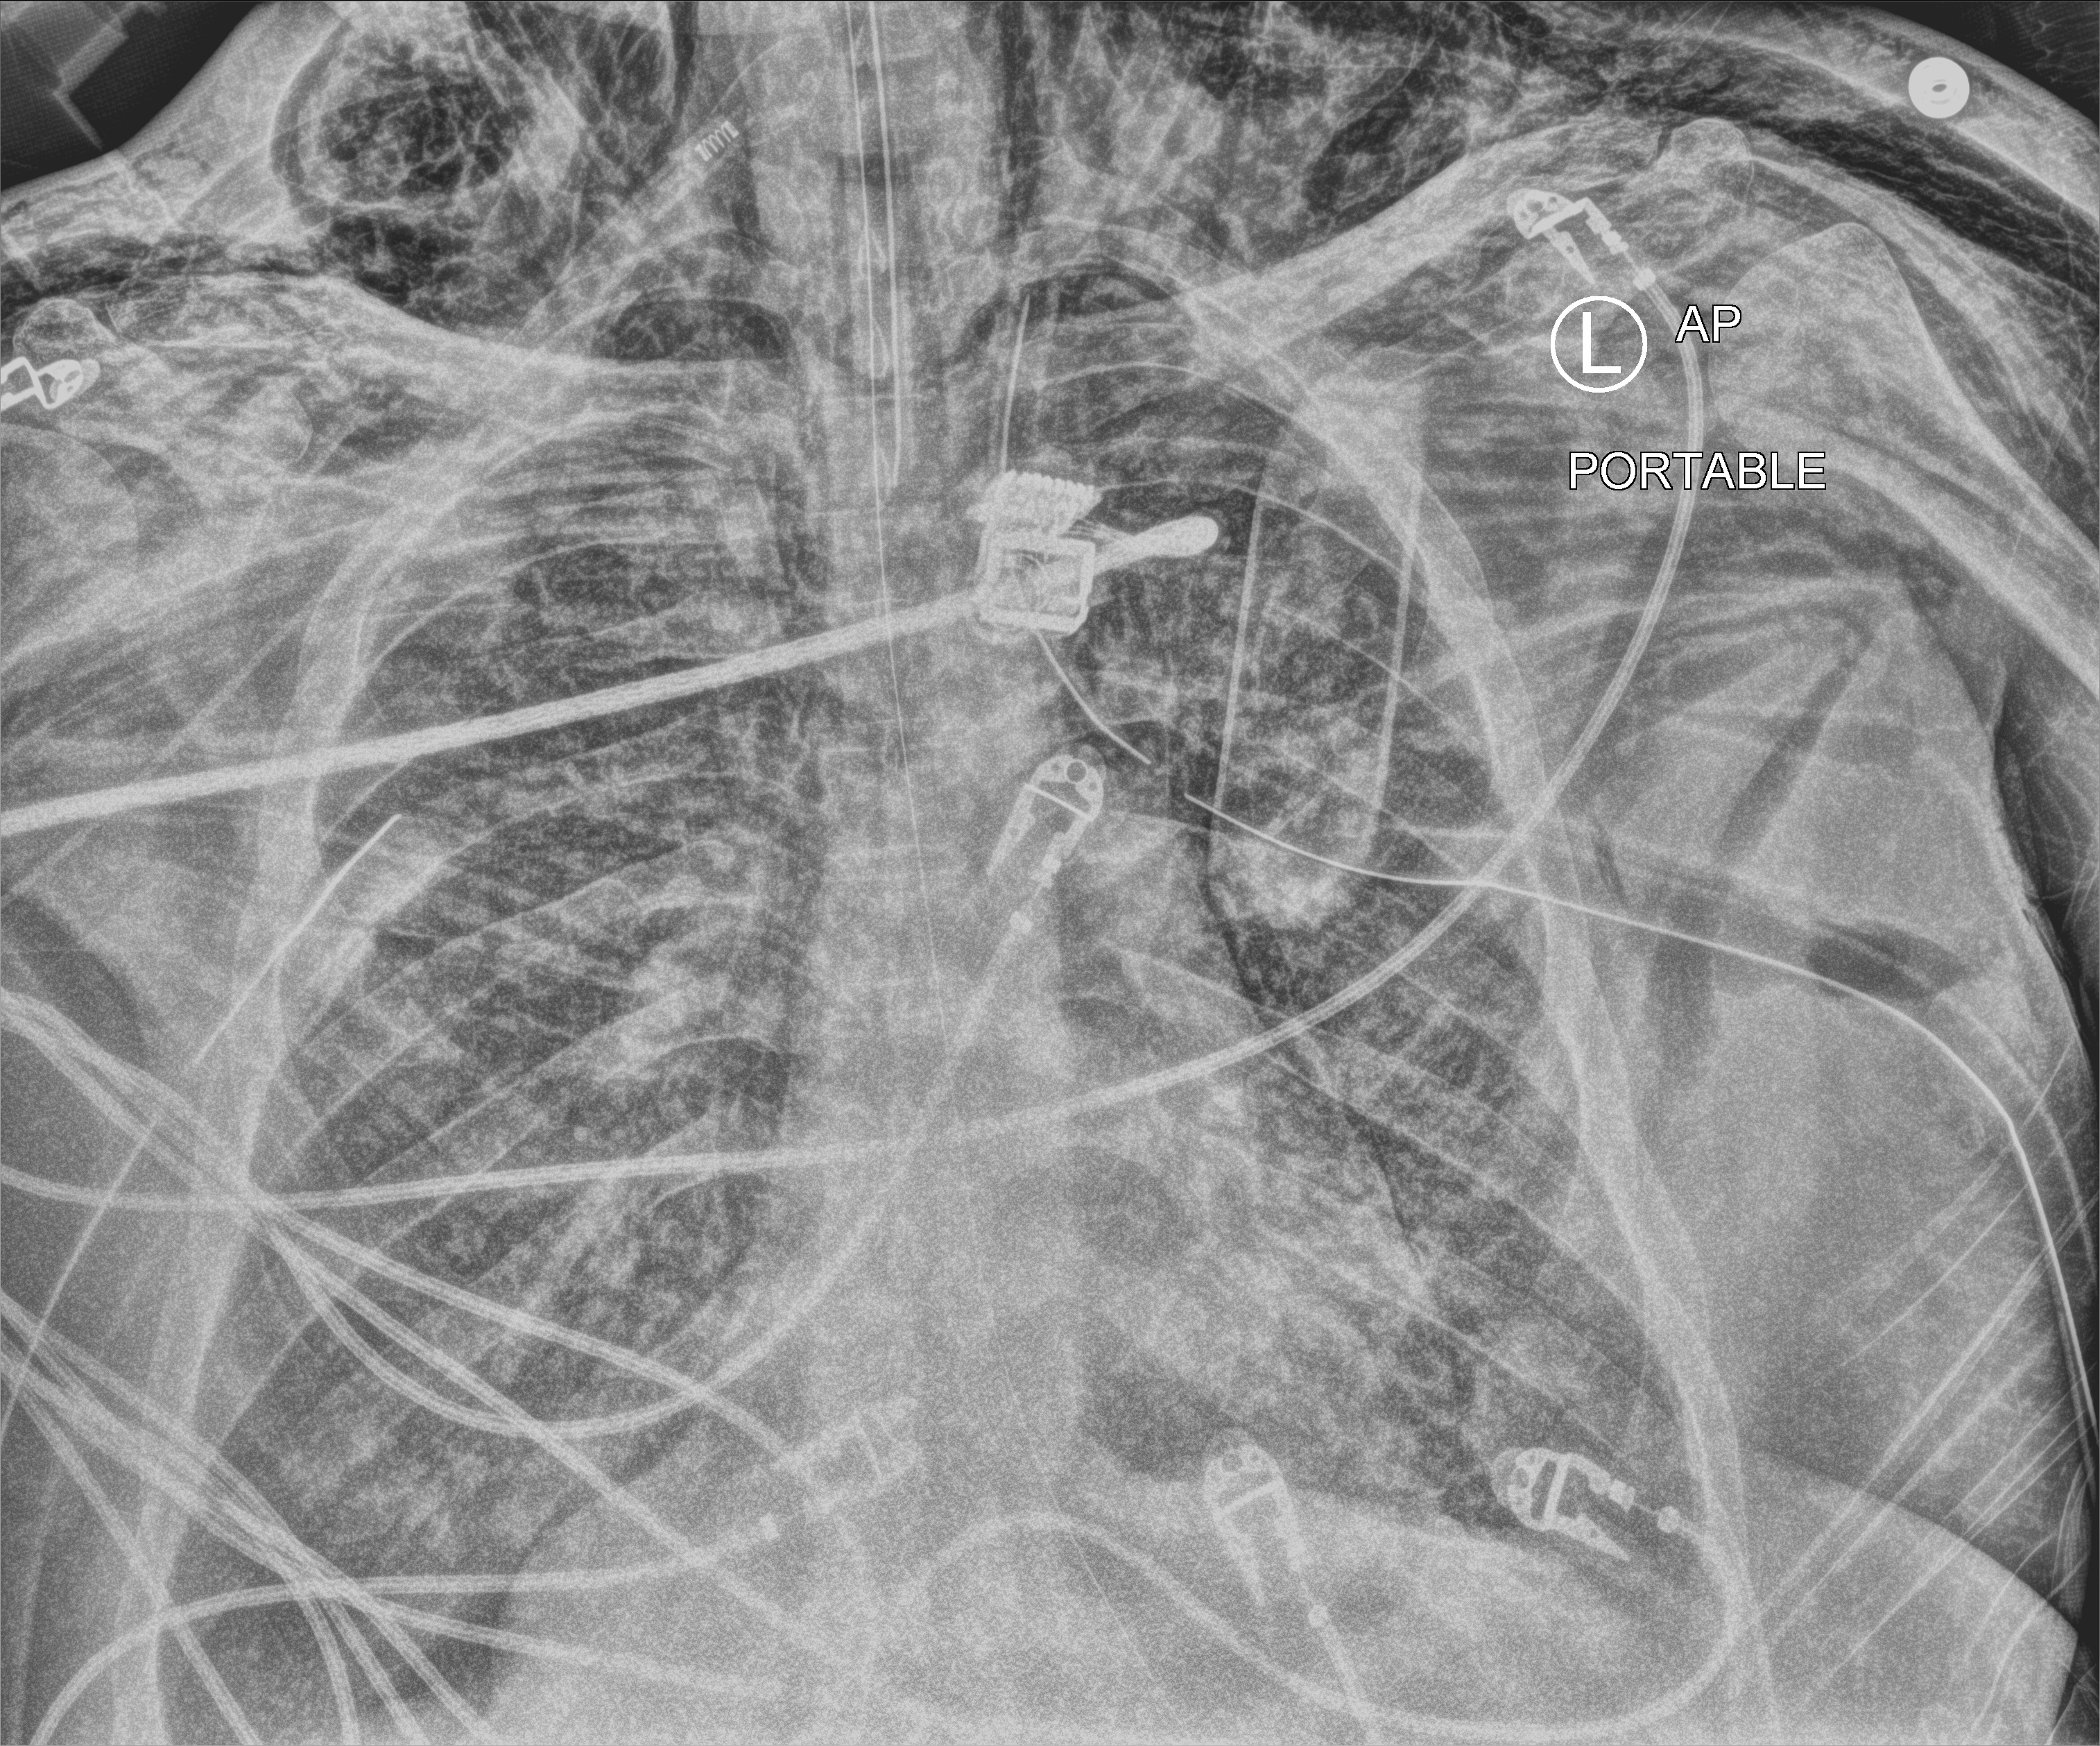
Chest X-ray (portable), anteroposterior (AP) projection. Adult patient hospitalised with COVID-19, age 18–59 years.
From the hospital-stay record, not from the radiograph (when in the stay this image was taken is not recorded):
- mechanically ventilated during this hospital stay: yes
- admitted to intensive care during this hospital stay: yes